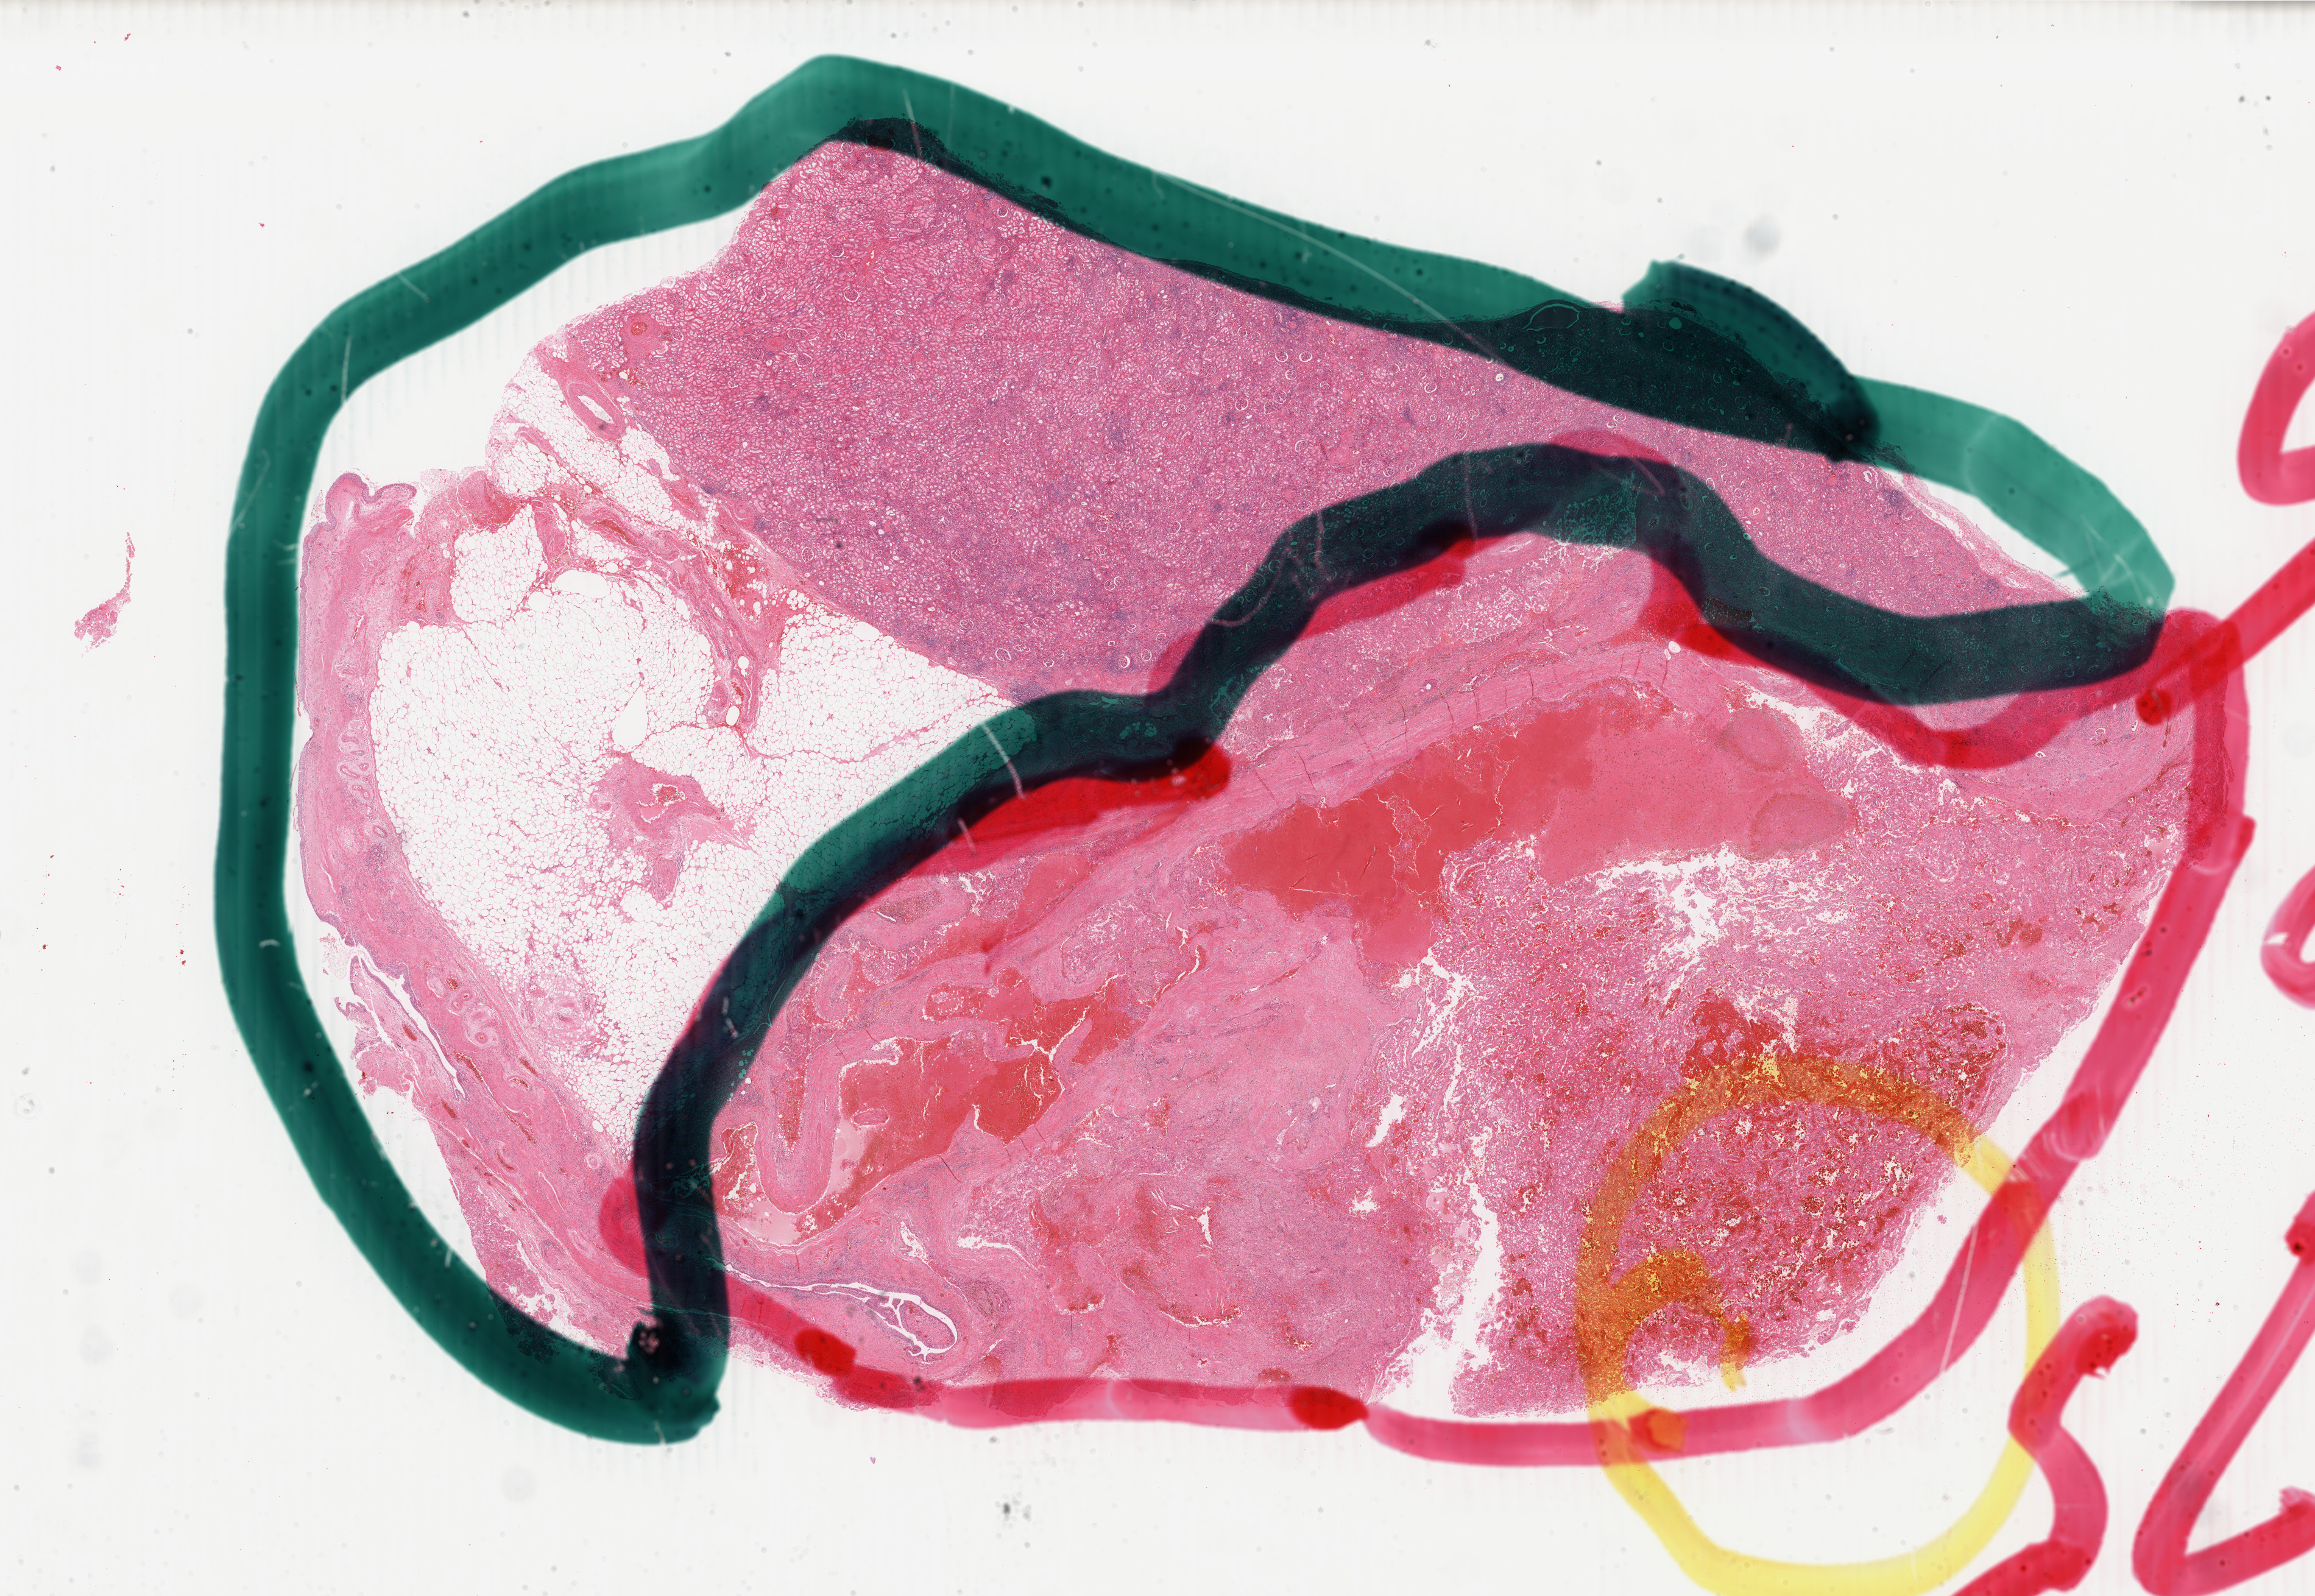
H&E-stained whole-slide image, whole scanned area (about 30.2 x 20.8 mm, from a 40x scan) shown as a low-resolution overview. Formalin-fixed paraffin-embedded (FFPE) diagnostic section. Sample: primary tumour, kidney. Patient: male, age at initial diagnosis 79 years.
Histologic diagnosis: Papillary adenocarcinoma, NOS.